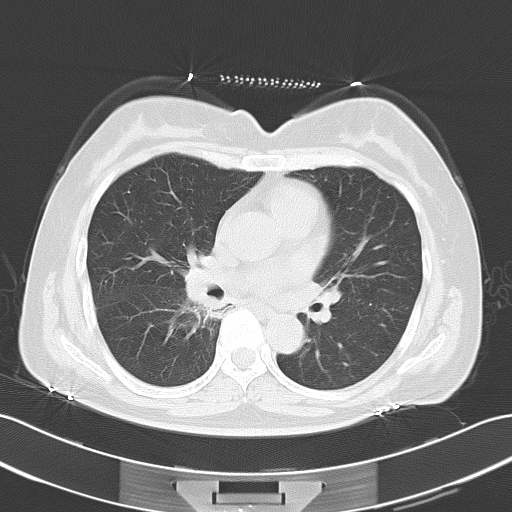
Chest CT, one axial slice. Position 30 of 55 along the scan axis. 120 kVp. Lung window (W 1500 / L -600 HU). 5 mm slice thickness. 512 × 512 image matrix, field of view 353 × 353 mm. Patient: female, 59 years. Case-level facts recorded for this patient, not image findings: clinical TNM (as recorded): T1c N0 M1b.
Structures marked on this image (bounding box drawn by a radiologist):
- lung tumour (recorded histology: adenocarcinoma): bounding box (x1, y1, x2, y2) in pixels: (190, 296, 226, 339)